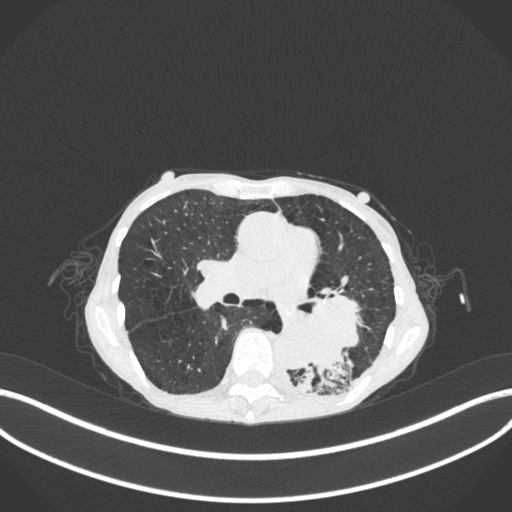
Chest CT, one axial slice. Position 146 of 347 along the scan axis. Reconstruction kernel B31f. Lung window (W 1500 / L -600 HU). 512 × 512 image matrix. Patient: female, 70 years. From the clinical record (not read from this slice): clinical TNM (as recorded): T3 N0 M0; histopathological grade: G3.
Structures marked on this image (rectangle marked by the reading radiologist):
- lung tumour (recorded histology: small cell carcinoma): box from (x=292, y=284) to (x=365, y=379) px